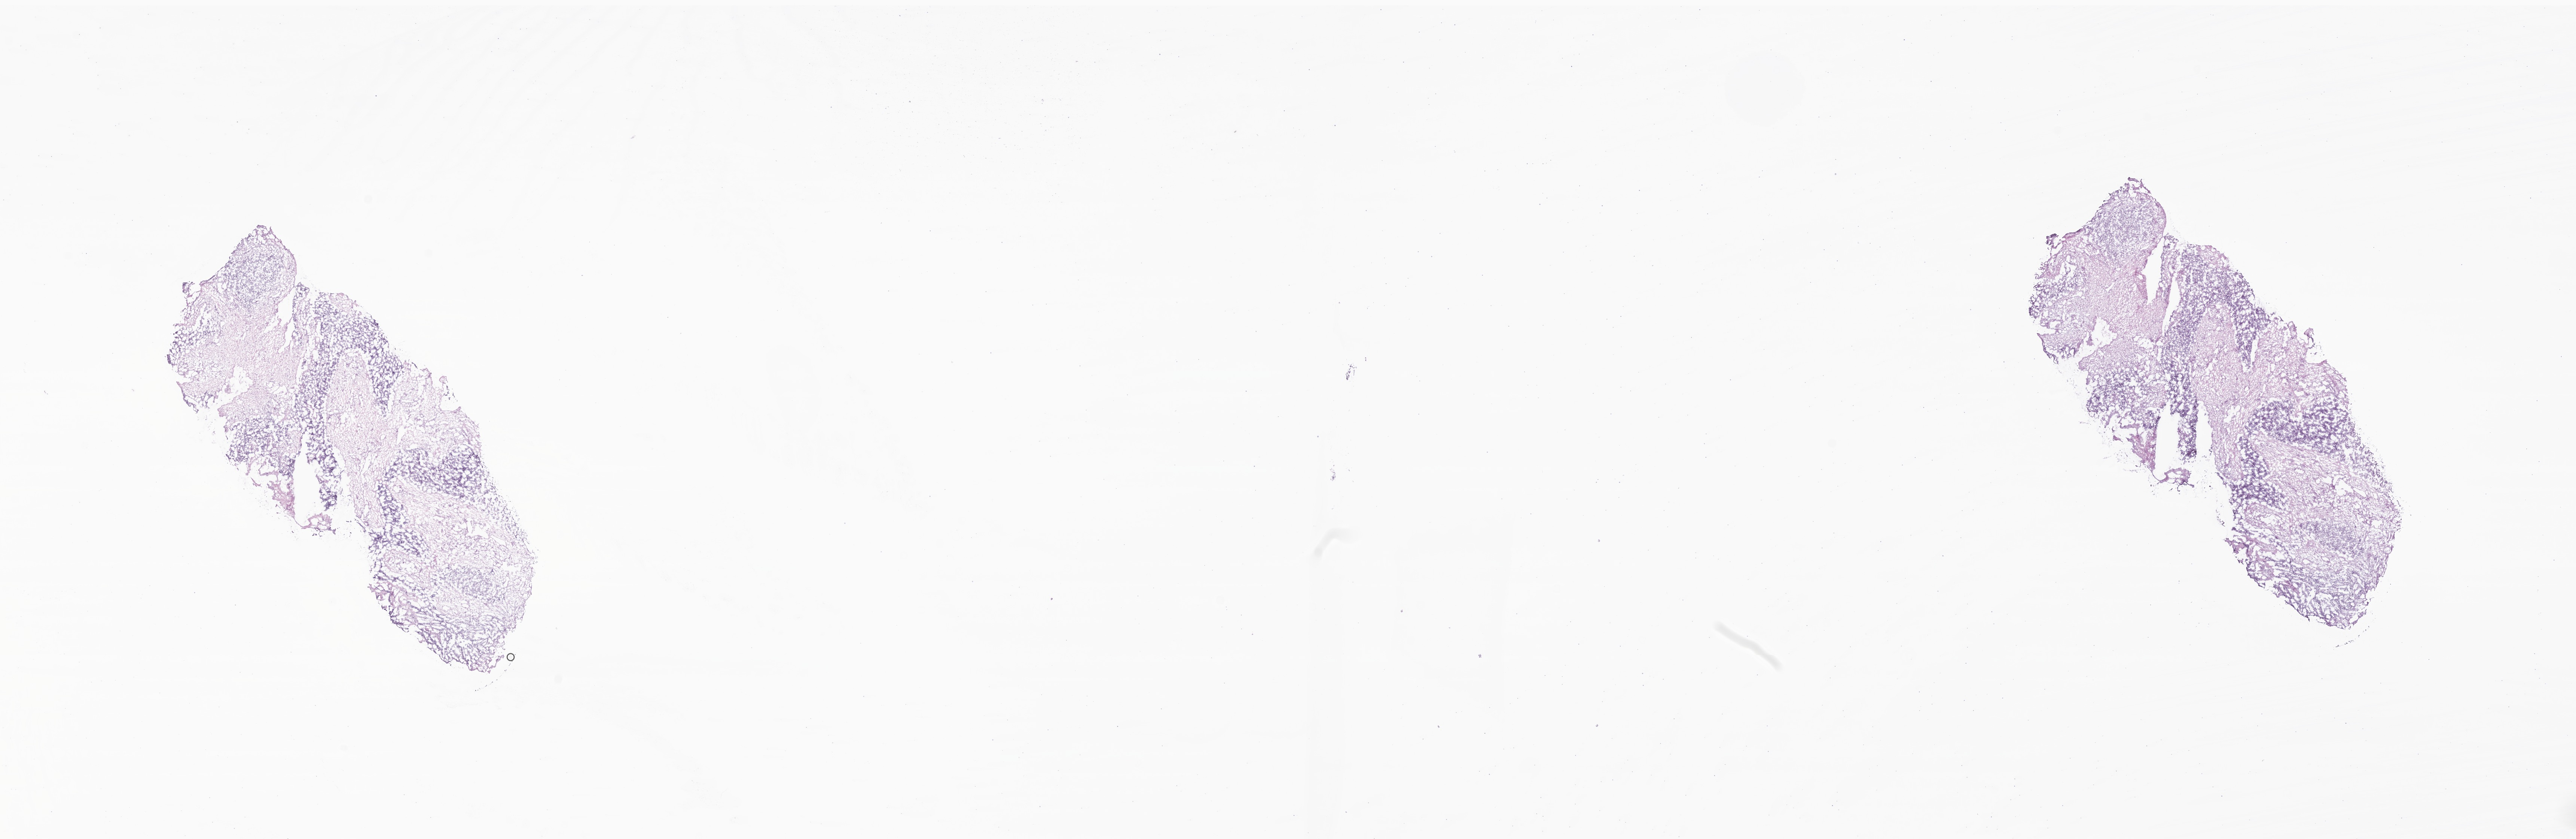
Whole-slide image, haematoxylin and eosin stain of tumor tissue from the head and neck, low-resolution overview of the scanned area, about 29.0 x 9.4 mm; frozen section. Patient female; age 97 months (8 years 1 month).
Diagnosis (ICD-O-3 morphology term): Rhabdomyosarcoma, NOS.